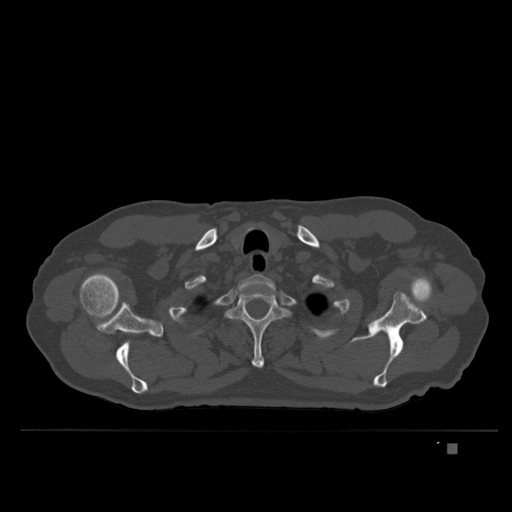
CT including the spine, one axial slice; bone window (W 1800 / L 400 HU); 1.5 mm slice thickness; 512 × 512 image matrix, field of view 434 × 434 mm. Male patient, age 73 years. Case-level facts recorded for this patient, not image findings: primary cancer: skin.
Annotated regions visible in this slice (semi-automatically segmented with operator editing):
- T1 vertebra: bounding box [x1, y1, x2, y2] px = [237, 274, 275, 289]
- T2 vertebra: [226, 293, 290, 368]